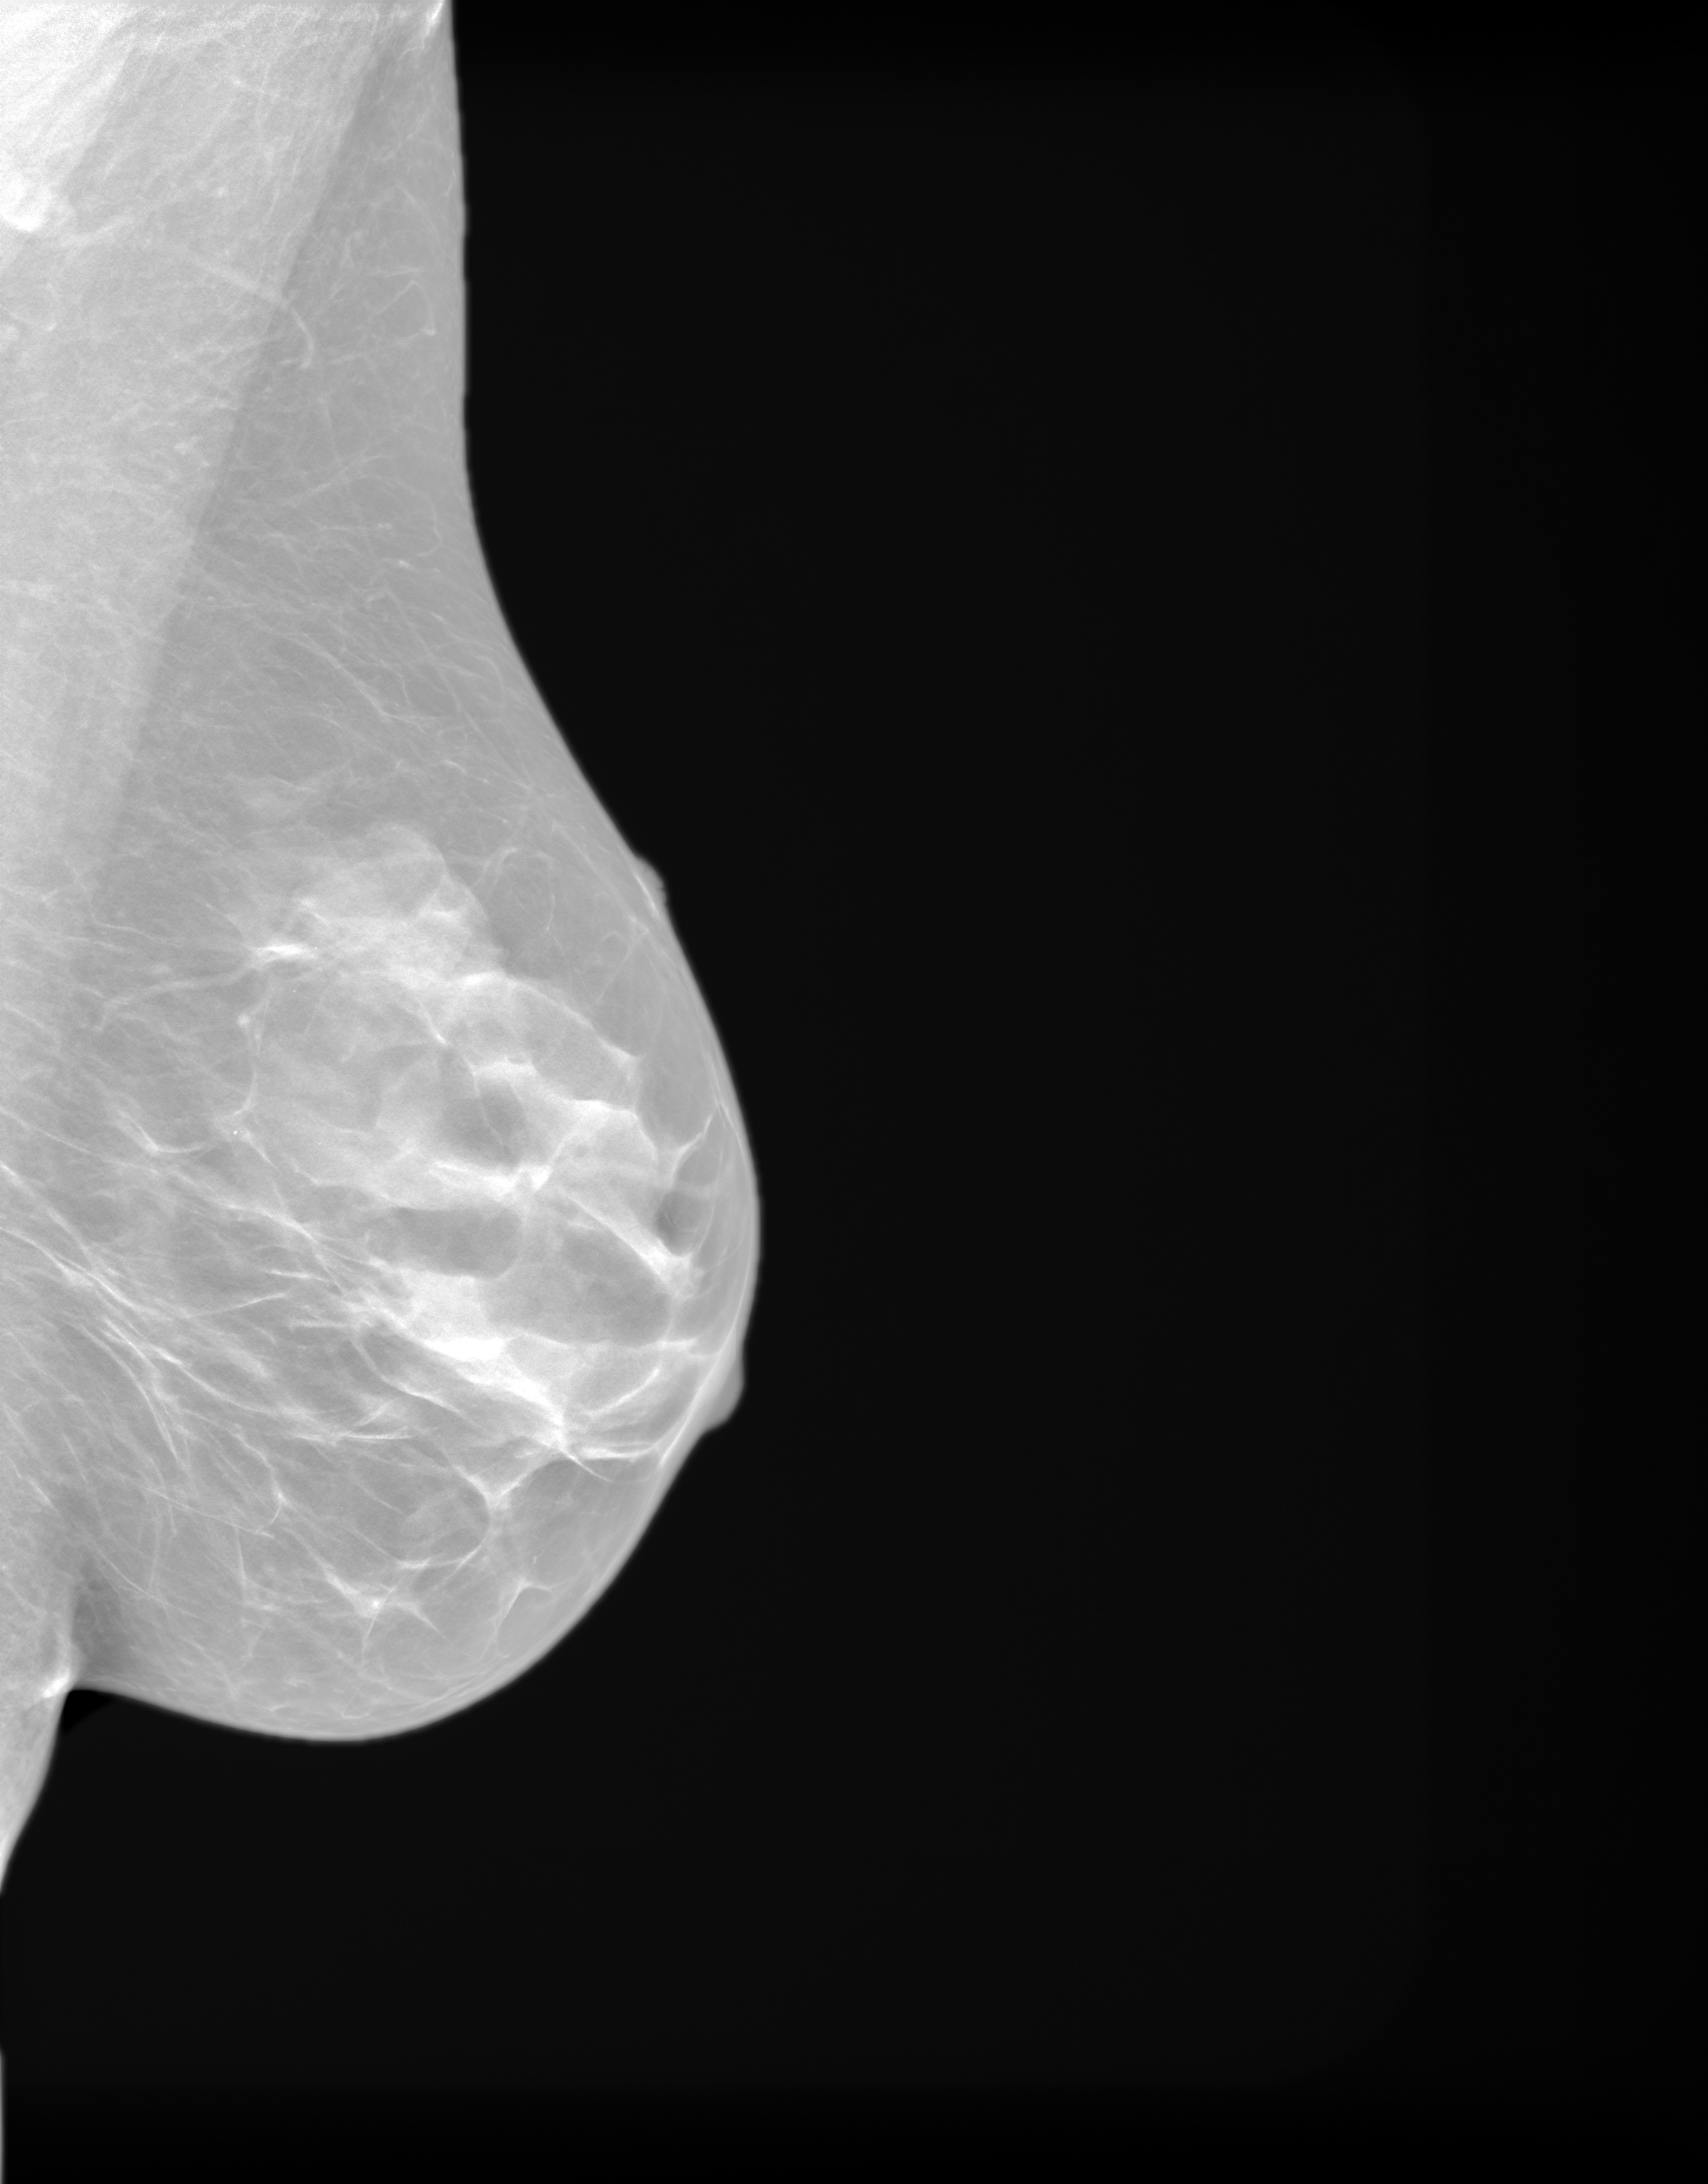
Synthetic 2-D view generated from a tomosynthesis acquisition (not an FFDM exposure); left breast; mediolateral oblique (MLO) view; annual screening mammography examination. Female patient, age 51 years.
Breast density at the screening exam (both breasts): heterogeneously dense (BI-RADS density category c). Final BI-RADS assessment for this screening round (tomosynthesis exam, both breasts): category 1. Recall: no recall after this screen.